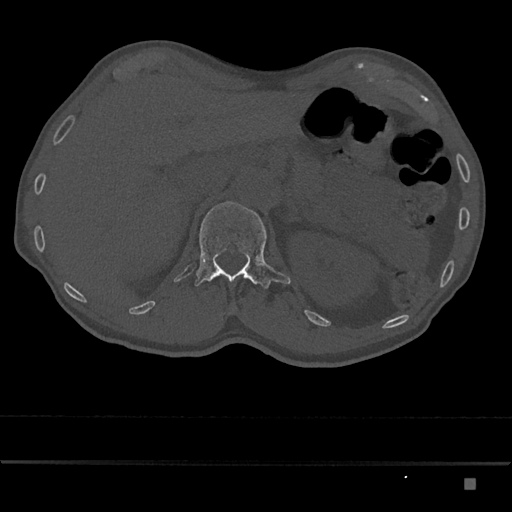
CT including the spine, one axial slice; slice 553 of 797 in the series (ordered by position); reconstruction kernel Br40s/3; 120 kVp; bone window (W 1800 / L 400 HU); 0.5 mm slice thickness; 512 × 512 image matrix, field of view 390 × 390 mm. Patient: male, 72 years. Case-level facts recorded for this patient, not image findings: primary cancer: prostate.
Annotated regions visible in this slice (semi-automatic segmentation, software-assisted and operator-edited):
- L1 vertebra: bounding box [x1, y1, x2, y2] px = [195, 201, 291, 289]